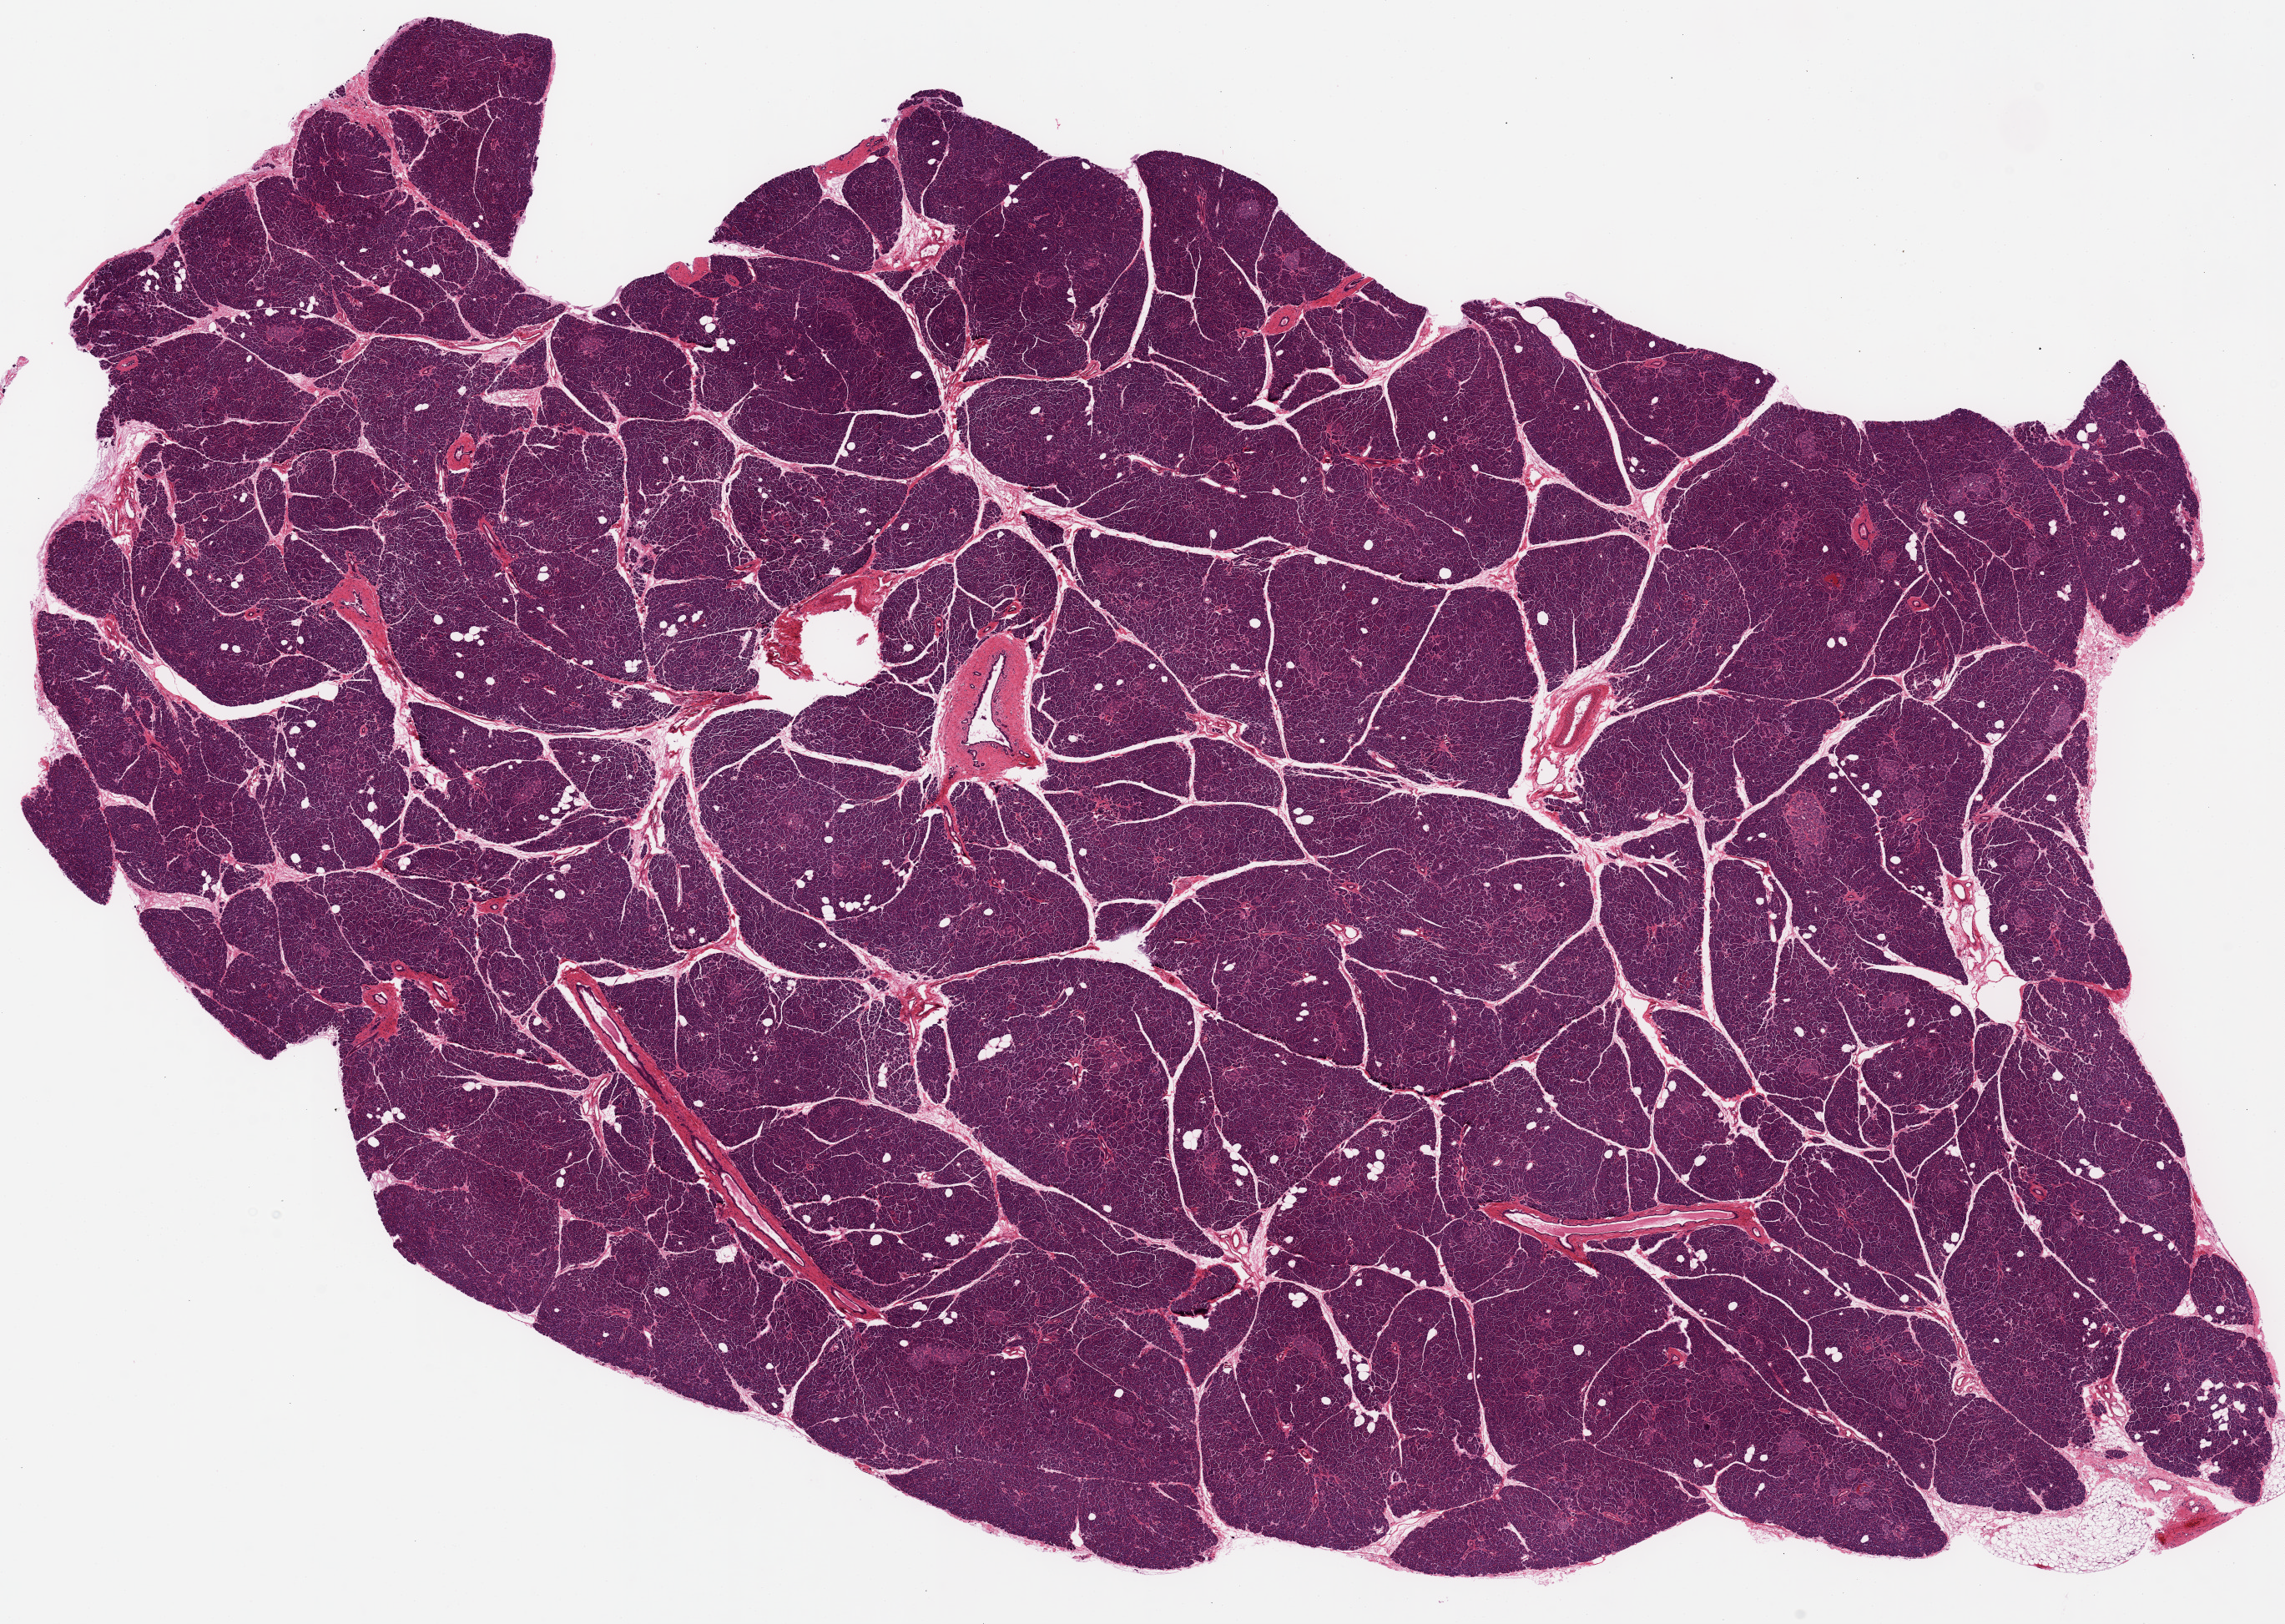
Whole-slide image, H&E stain, low-resolution overview of the scanned area, about 21.7 x 15.4 mm, PAXgene-fixed paraffin-embedded (PFPE) section, target tissue: pancreas, donor tissue sample. Male donor.
Pathologist's review note for this sample: large aliquot 20.5 x 12.8.